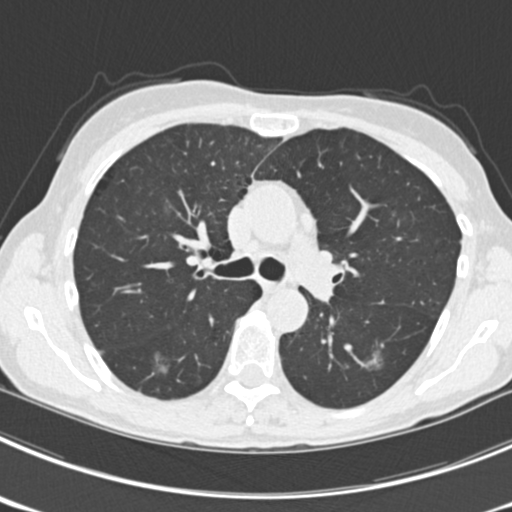
Axial slice from a low-dose chest CT screening exam, third screening round (two years after baseline), lung window (W 1500 / L -600 HU), 2 mm slice thickness, standard (soft-tissue) reconstruction kernel (B30f), slice 75 of 225 in the series, 512 × 512 image matrix. Female participant, aged 63 years at enrolment.
- 2 lesions marked by an expert reader on this slice (largest first), box from (x=135, y=337) to (x=179, y=382) px; (x=357, y=344)–(x=398, y=382).
- The screening reader recorded 9 non-calcified nodules or masses ≥4 mm on this exam; which of them these boxes mark is not recorded.